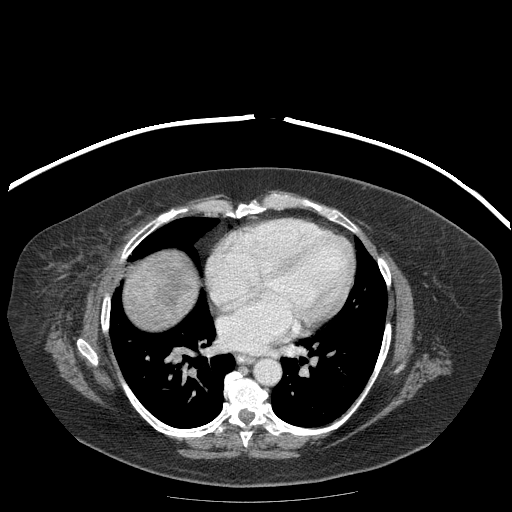
Contrast-enhanced abdominal CT (liver protocol), one axial slice; slice 185 of 204 in the series (ordered by position); reconstruction kernel STANDARD; 120 kVp; soft-tissue window (W 400 / L 40 HU); 2.5 mm slice thickness; 512 × 512 image matrix, field of view 440 × 440 mm. From the clinical record (not read from this slice): diagnosis: hepatocellular carcinoma (patient treated with transarterial chemoembolisation; whether this scan precedes or follows treatment is not stated here); TNM stage (as recorded): Stage-IIIB; Child-Pugh class: A.
Structures marked on this image (semi-automatically segmented with operator editing):
- liver parenchyma outside the tumour (the mass and vessels are separate outlines, so this box may not span the whole liver): box from (x=124, y=250) to (x=196, y=330) px
- mass: (x=147, y=256)–(x=195, y=318)